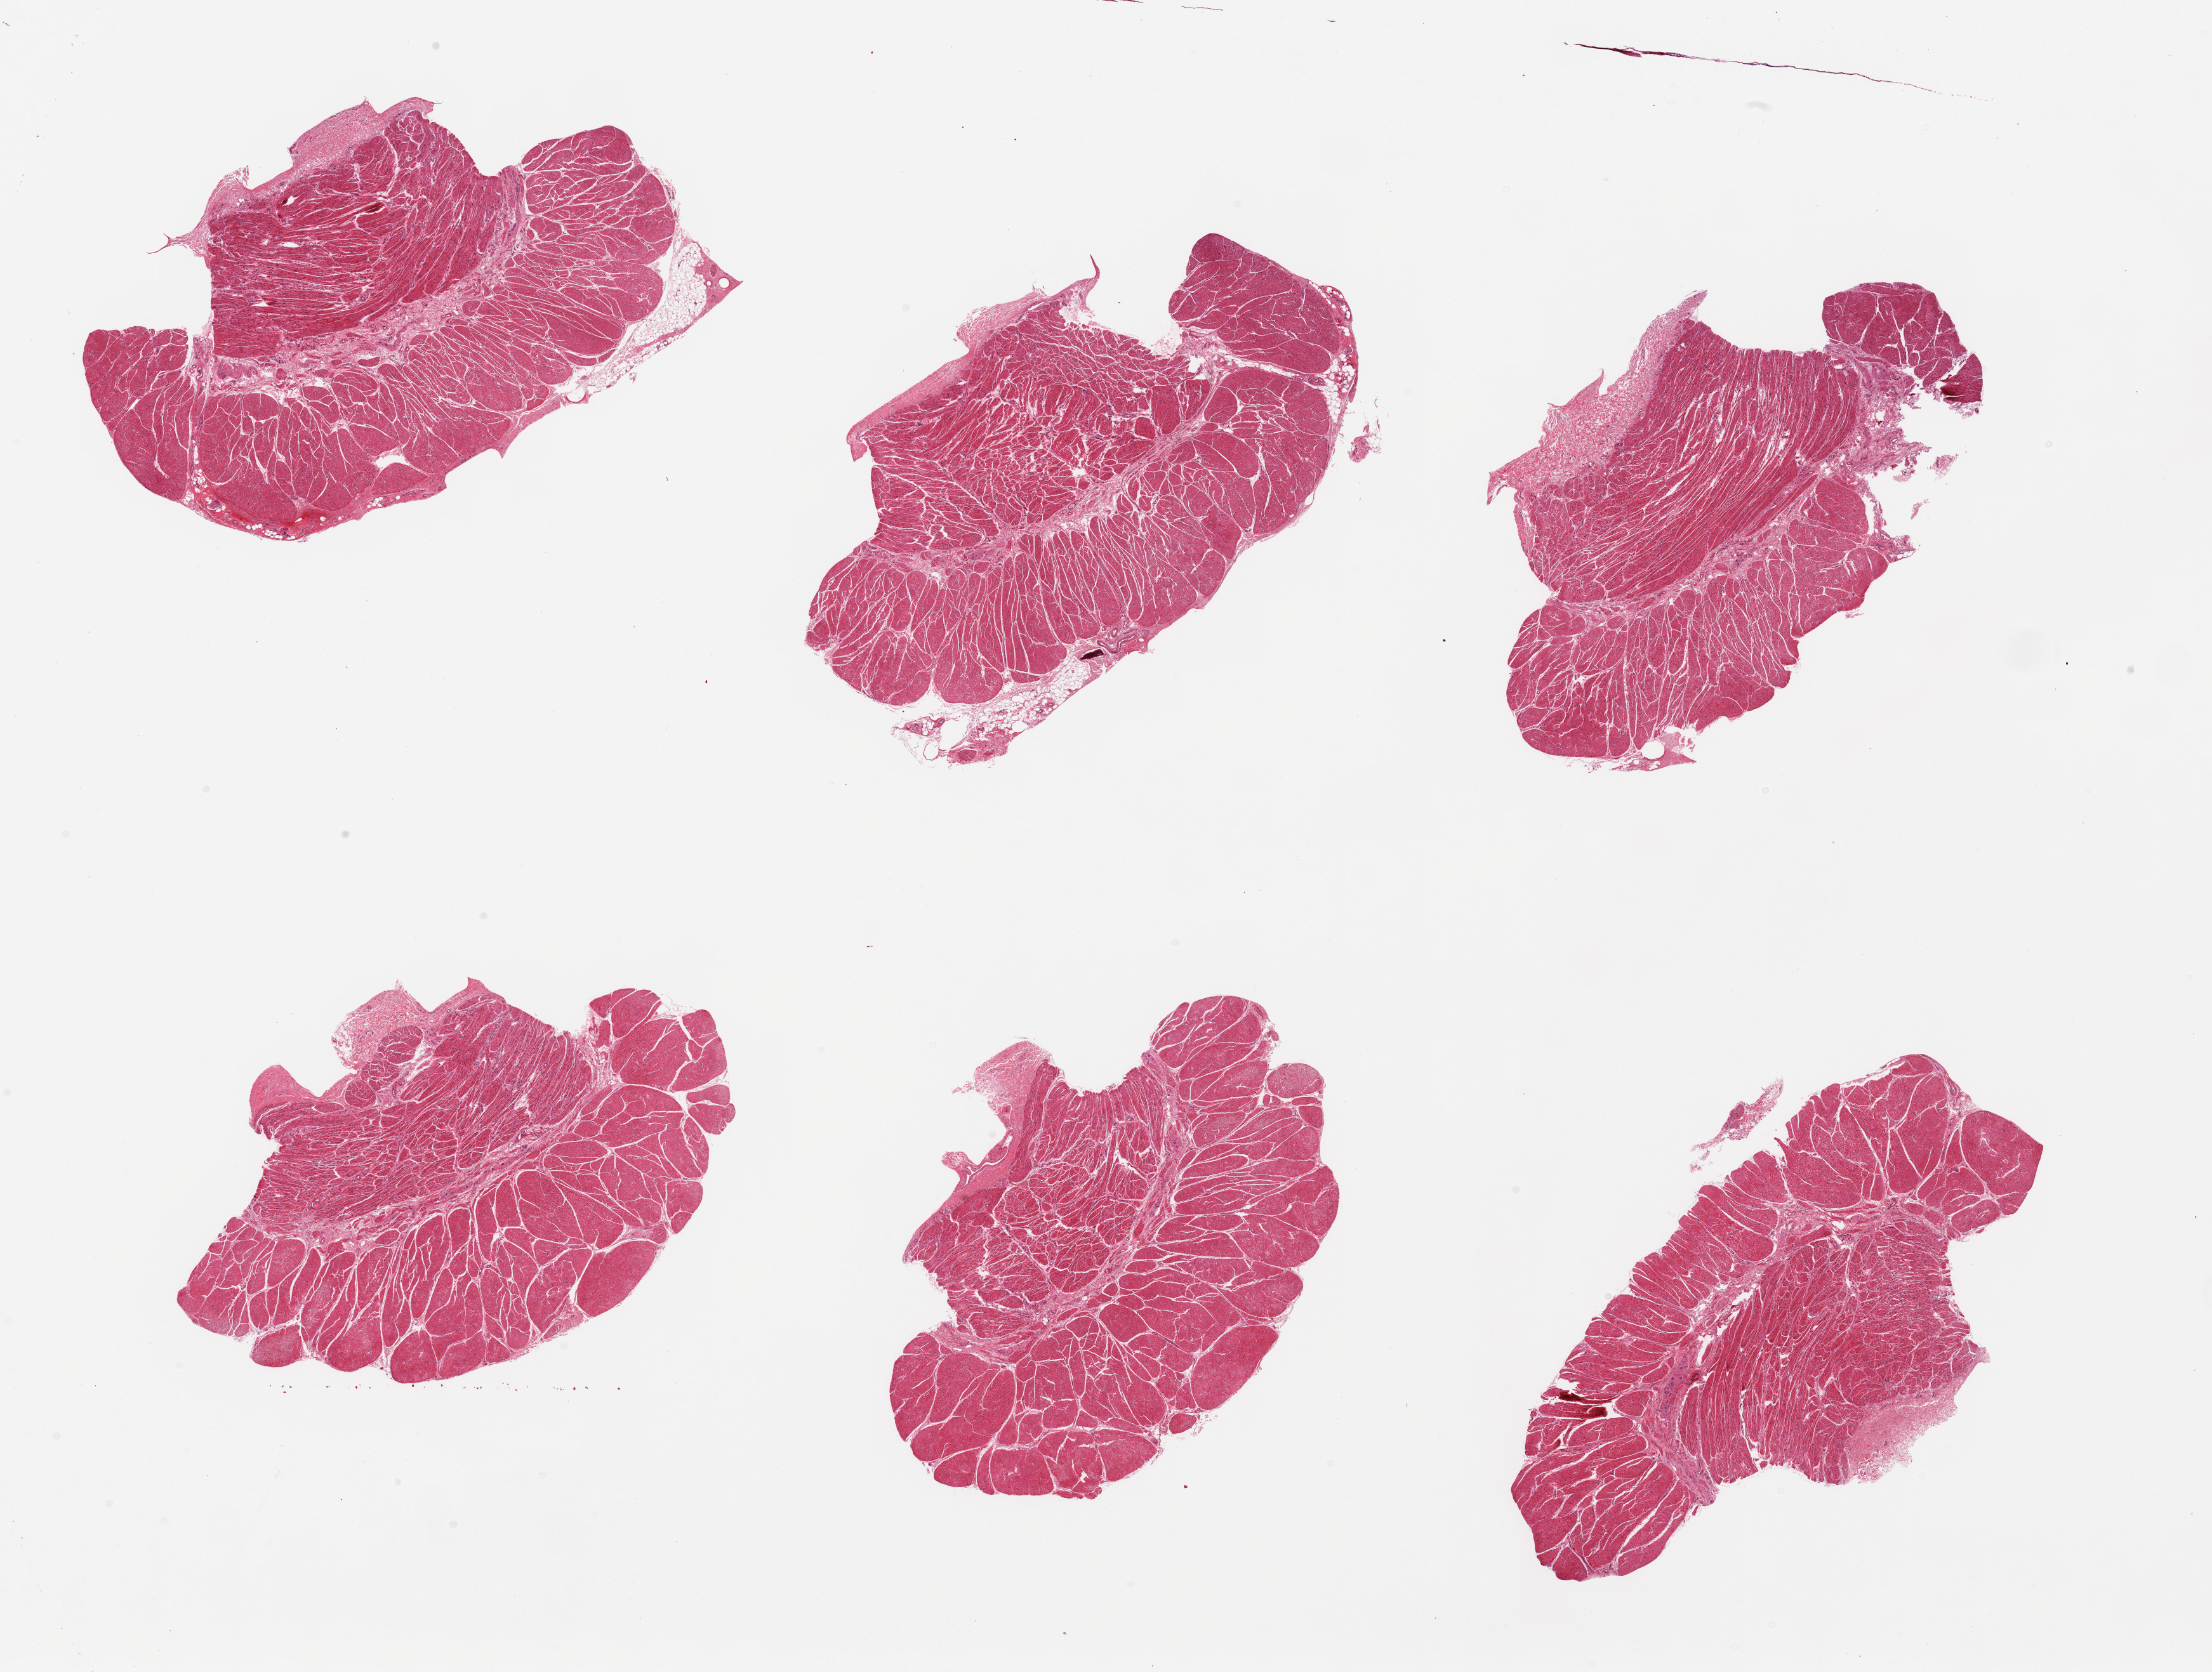
Digitized hematoxylin and eosin (H&E)-stained section, brightfield, whole scanned area (about 27.6 x 20.8 mm, from a 20x scan) shown as a low-resolution overview; PAXgene-fixed, paraffin-embedded tissue; section of esophageal muscle (target tissue); donor tissue sample. Male donor.
Pathologist's review note for this sample: 6 pieces; well preserved, well dissected.